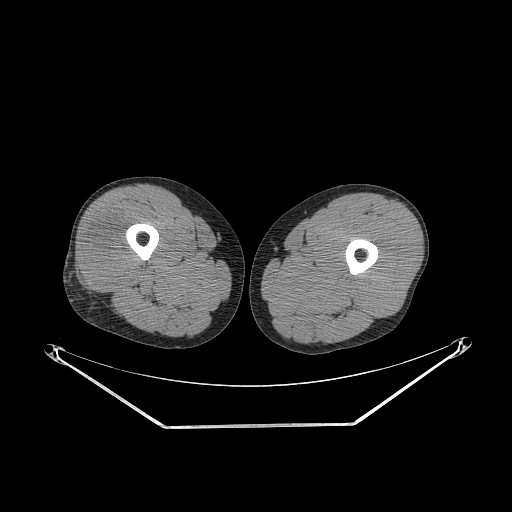
CT of an extremity soft-tissue mass (from a PET/CT study), one axial slice. Position 236 of 267 along the scan axis. Reconstruction kernel STANDARD. Soft-tissue window (W 400 / L 40 HU). 3.75 mm slice thickness. 512 × 512 image matrix, field of view 500 × 500 mm. Male patient. Case-level facts recorded for this patient, not image findings: histological type: poorly differentiated synovial sarcoma; grade: high; site of the primary tumour: right buttock.
Structures marked on this image (expert contour drawn on MRI and transferred to this co-registered scan by the dataset authors):
- gross tumour volume including surrounding oedema: bounding box (x1, y1, x2, y2) in pixels: (82, 219, 133, 289)
- gross tumour volume (mass): (85, 228, 133, 289)